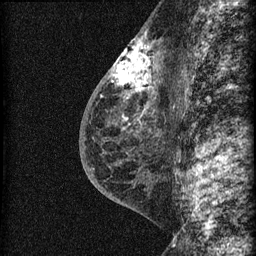
Breast MRI (dynamic contrast-enhanced), one sagittal slice. Position 33 of 60 along the scan axis. Dynamic contrast-enhanced series, image 2 of 3 at this slice position (ordered by acquisition). 1.5 T. TE 4.2 ms, TR 22.7 ms. 1.5 mm slice thickness. 256 × 256 image matrix, field of view 180 × 180 mm. Female patient, age 48 years. From the clinical record (not read from this slice): setting: breast cancer imaged before/during neoadjuvant chemotherapy; receptor status: triple-negative.
Annotated regions visible in this slice (semi-automatically segmented with operator editing):
- analysis volume of interest (the breast-tissue region the enhancement analysis was run in; not a lesion): bounding box <115,34,169,162> (left, top, right, bottom; pixels)
- tumour enhancement mask (voxels above the 90 % enhancement threshold inside the analysis volume of interest): <115,35,154,92>